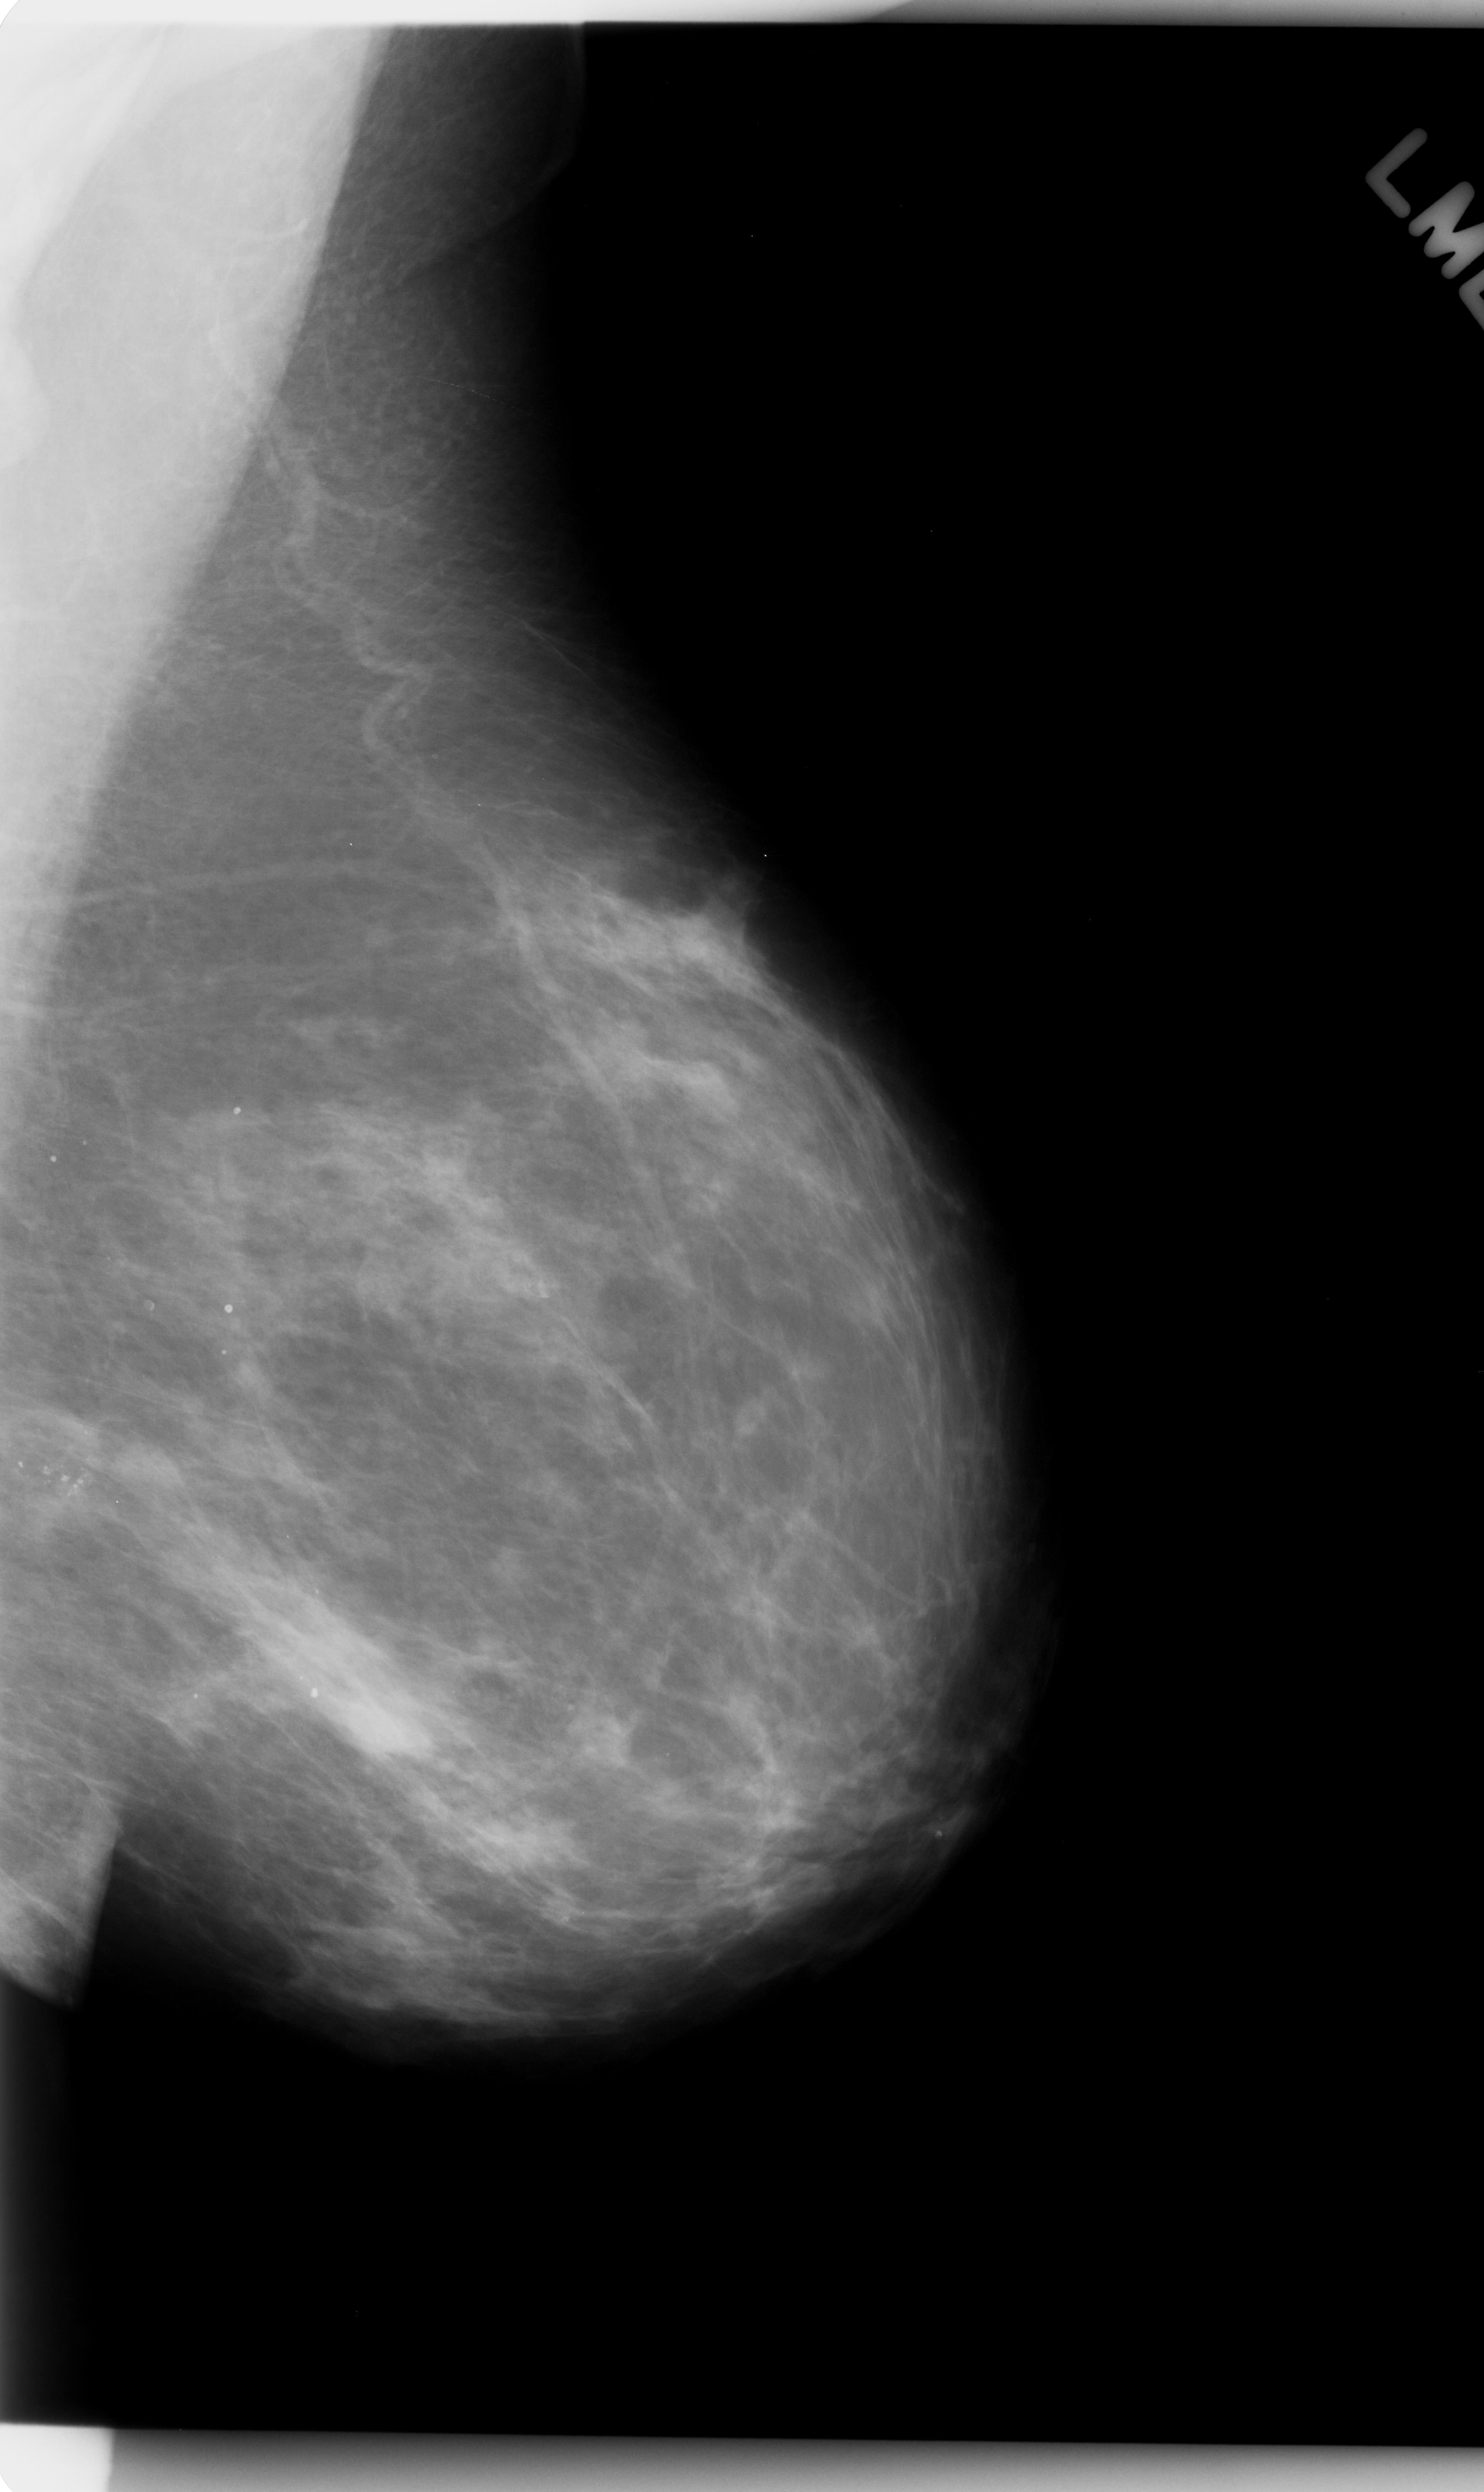
Scanned film-screen mammogram. Left breast. Mediolateral oblique (MLO) view. BI-RADS breast density category 2 (scale 1–4). 1484 × 2492 image matrix.
Expert-marked regions of interest on this film, with their recorded descriptors:
- calcifications, morphology amorphous, distribution clustered; BI-RADS assessment category 4; pathology result (as recorded, not read from the image): benign: bounding box [x1, y1, x2, y2] px = [0, 1370, 145, 1579]